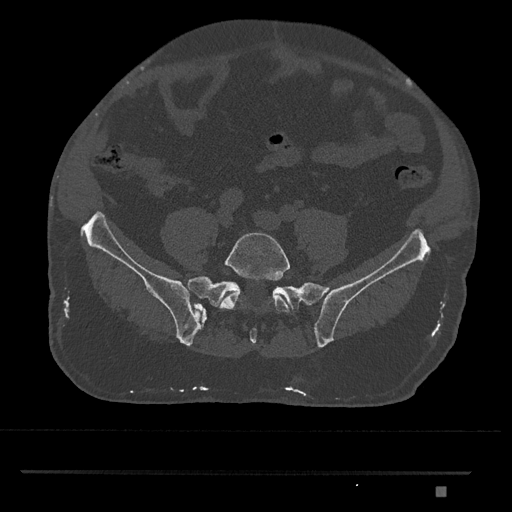
CT including the spine, one axial slice; position 535 of 1134 along the scan axis; reconstruction kernel Br40s/3; 120 kVp; bone window (W 1800 / L 400 HU); 512 × 512 image matrix. Patient: male, 65 years. Case-level facts recorded for this patient, not image findings: primary cancer: prostate.
Structures marked on this image (semi-automatic segmentation, software-assisted and operator-edited):
- L5 vertebra: bounding box [x1, y1, x2, y2] px = [219, 232, 290, 313]